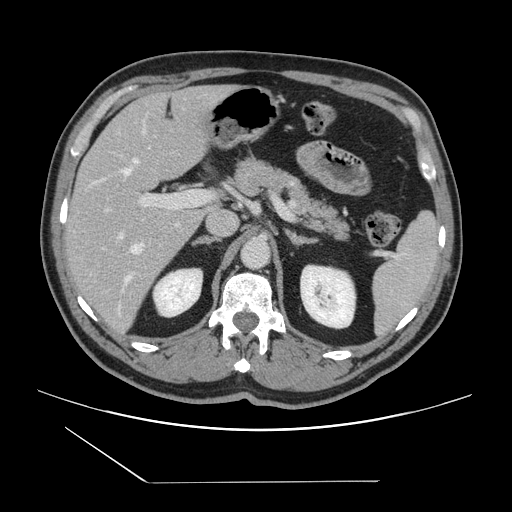
Contrast-enhanced abdominal CT, one axial slice; position 85 of 157 along the scan axis; 120 kVp; intravenous contrast given; soft-tissue window (W 400 / L 40 HU); 2.5 mm slice thickness; 512 × 512 image matrix, field of view 407 × 407 mm. Male patient, age 61 years. Case-level facts recorded for this patient, not image findings: diagnosis: colorectal cancer liver metastases, imaged before liver resection; multiple liver metastases: yes; largest metastasis: 5.5 cm; disease in both lobes: yes.
Outlined on this slice (outlined manually by an expert reader):
- hepatic veins: bounding box <122,129,145,283> (left, top, right, bottom; pixels)
- liver: <66,86,230,337>
- planned liver remnant (the part of the liver to remain after resection): <67,86,230,221>
- portal vein (with intrahepatic branches): <105,191,206,239>